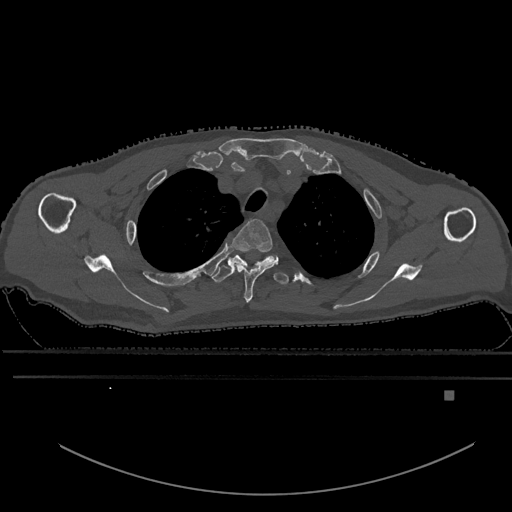
CT including the spine, one axial slice. Bone window (W 1800 / L 400 HU). 0.5 mm slice thickness. 512 × 512 image matrix, field of view 456 × 456 mm. Male patient, age 82 years. Case-level facts recorded for this patient, not image findings: primary cancer: prostate.
Structures marked on this image (semi-automatically segmented with operator editing):
- T2 vertebra: box from (x=231, y=219) to (x=279, y=303) px
- T3 vertebra: (x=211, y=254)–(x=289, y=285)